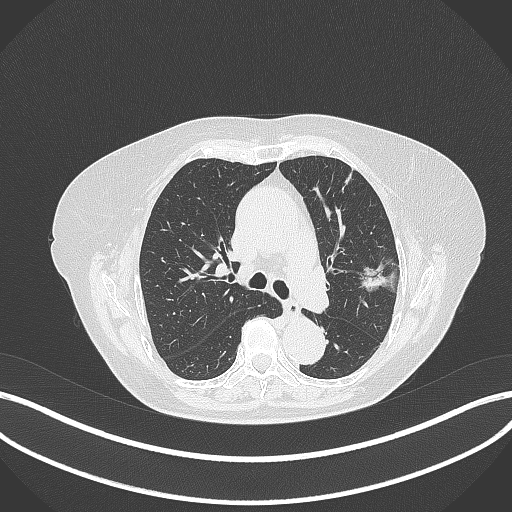
Chest CT, one axial slice. Position 210 of 316 along the scan axis. Reconstruction kernel B70f. 120 kVp. Lung window (W 1500 / L -600 HU). 512 × 512 image matrix. Patient: female, 75 years. From the clinical record (not read from this slice): clinical TNM (as recorded): T1c N0 M0.
Outlined on this slice (bounding box drawn by a radiologist):
- lung tumour (recorded histology: adenocarcinoma): bounding box [x1, y1, x2, y2] px = [358, 261, 386, 293]